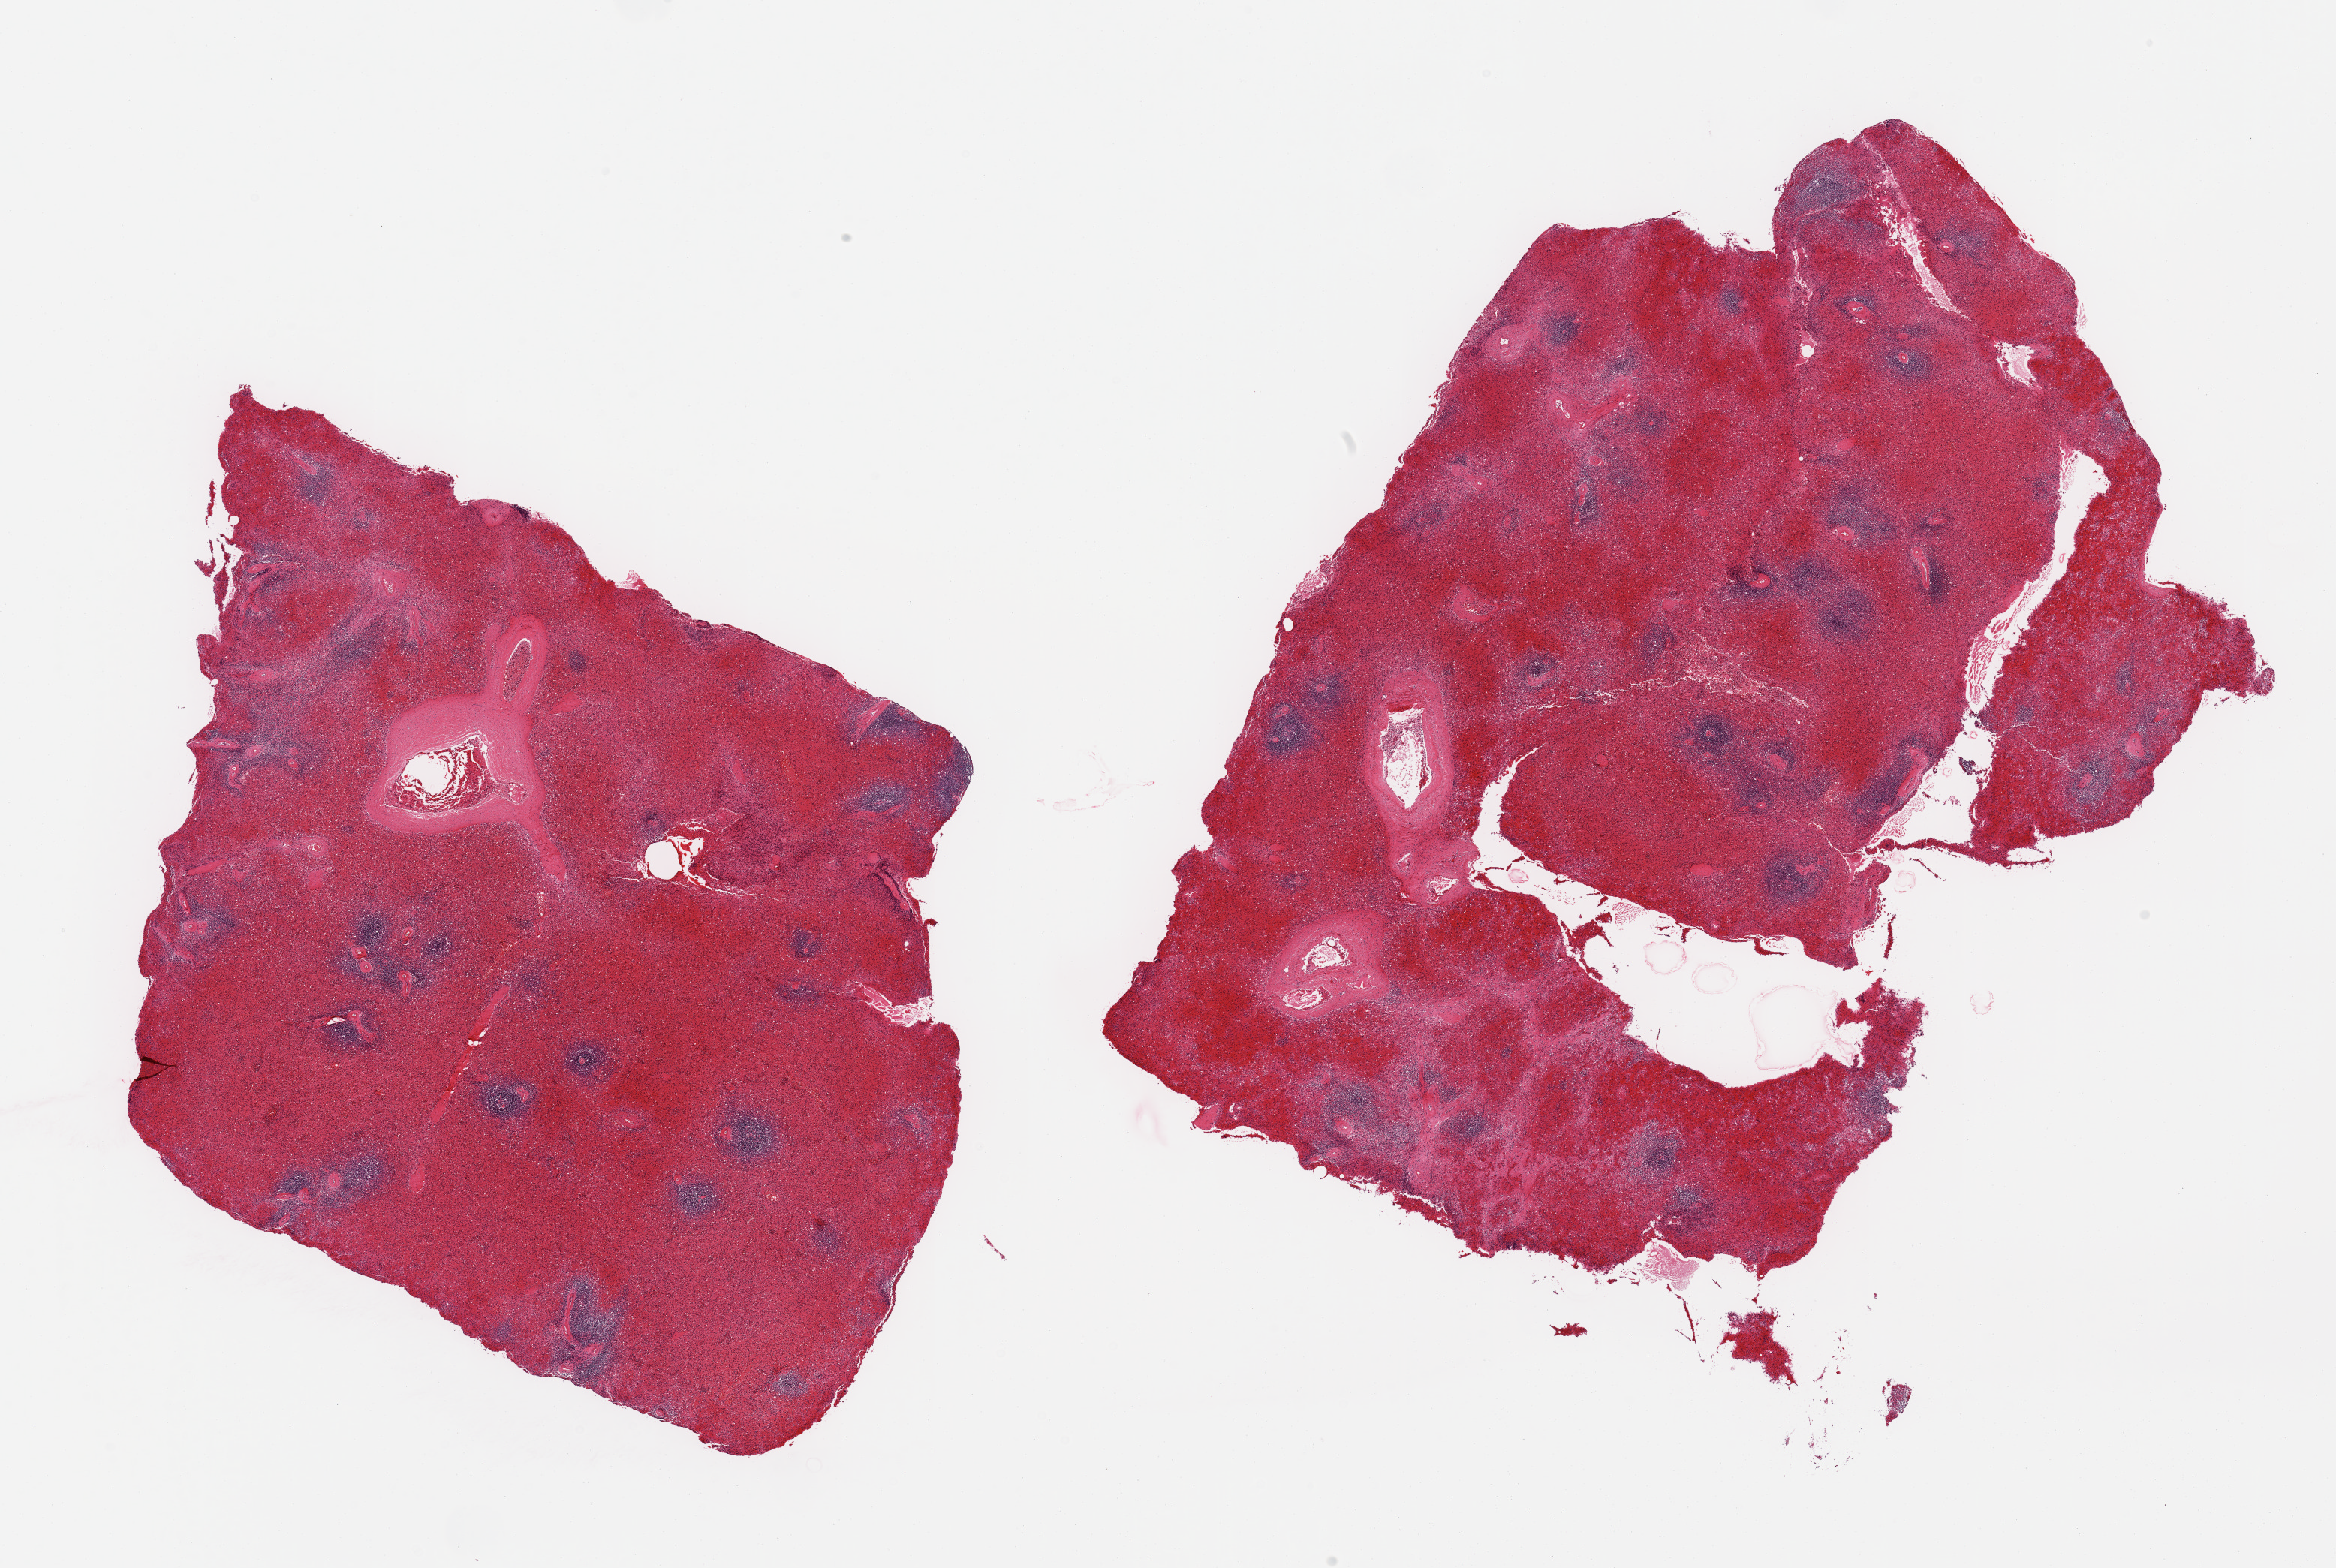
H&E whole-slide image — whole scanned area (about 24.6 x 16.5 mm) shown as a low-resolution overview, PAXgene-fixed, paraffin-embedded tissue, sampled site (target tissue): spleen, tissue donor sample. Male donor.
Reviewer comment on this tissue sample: 2 pieces, marked congestion.